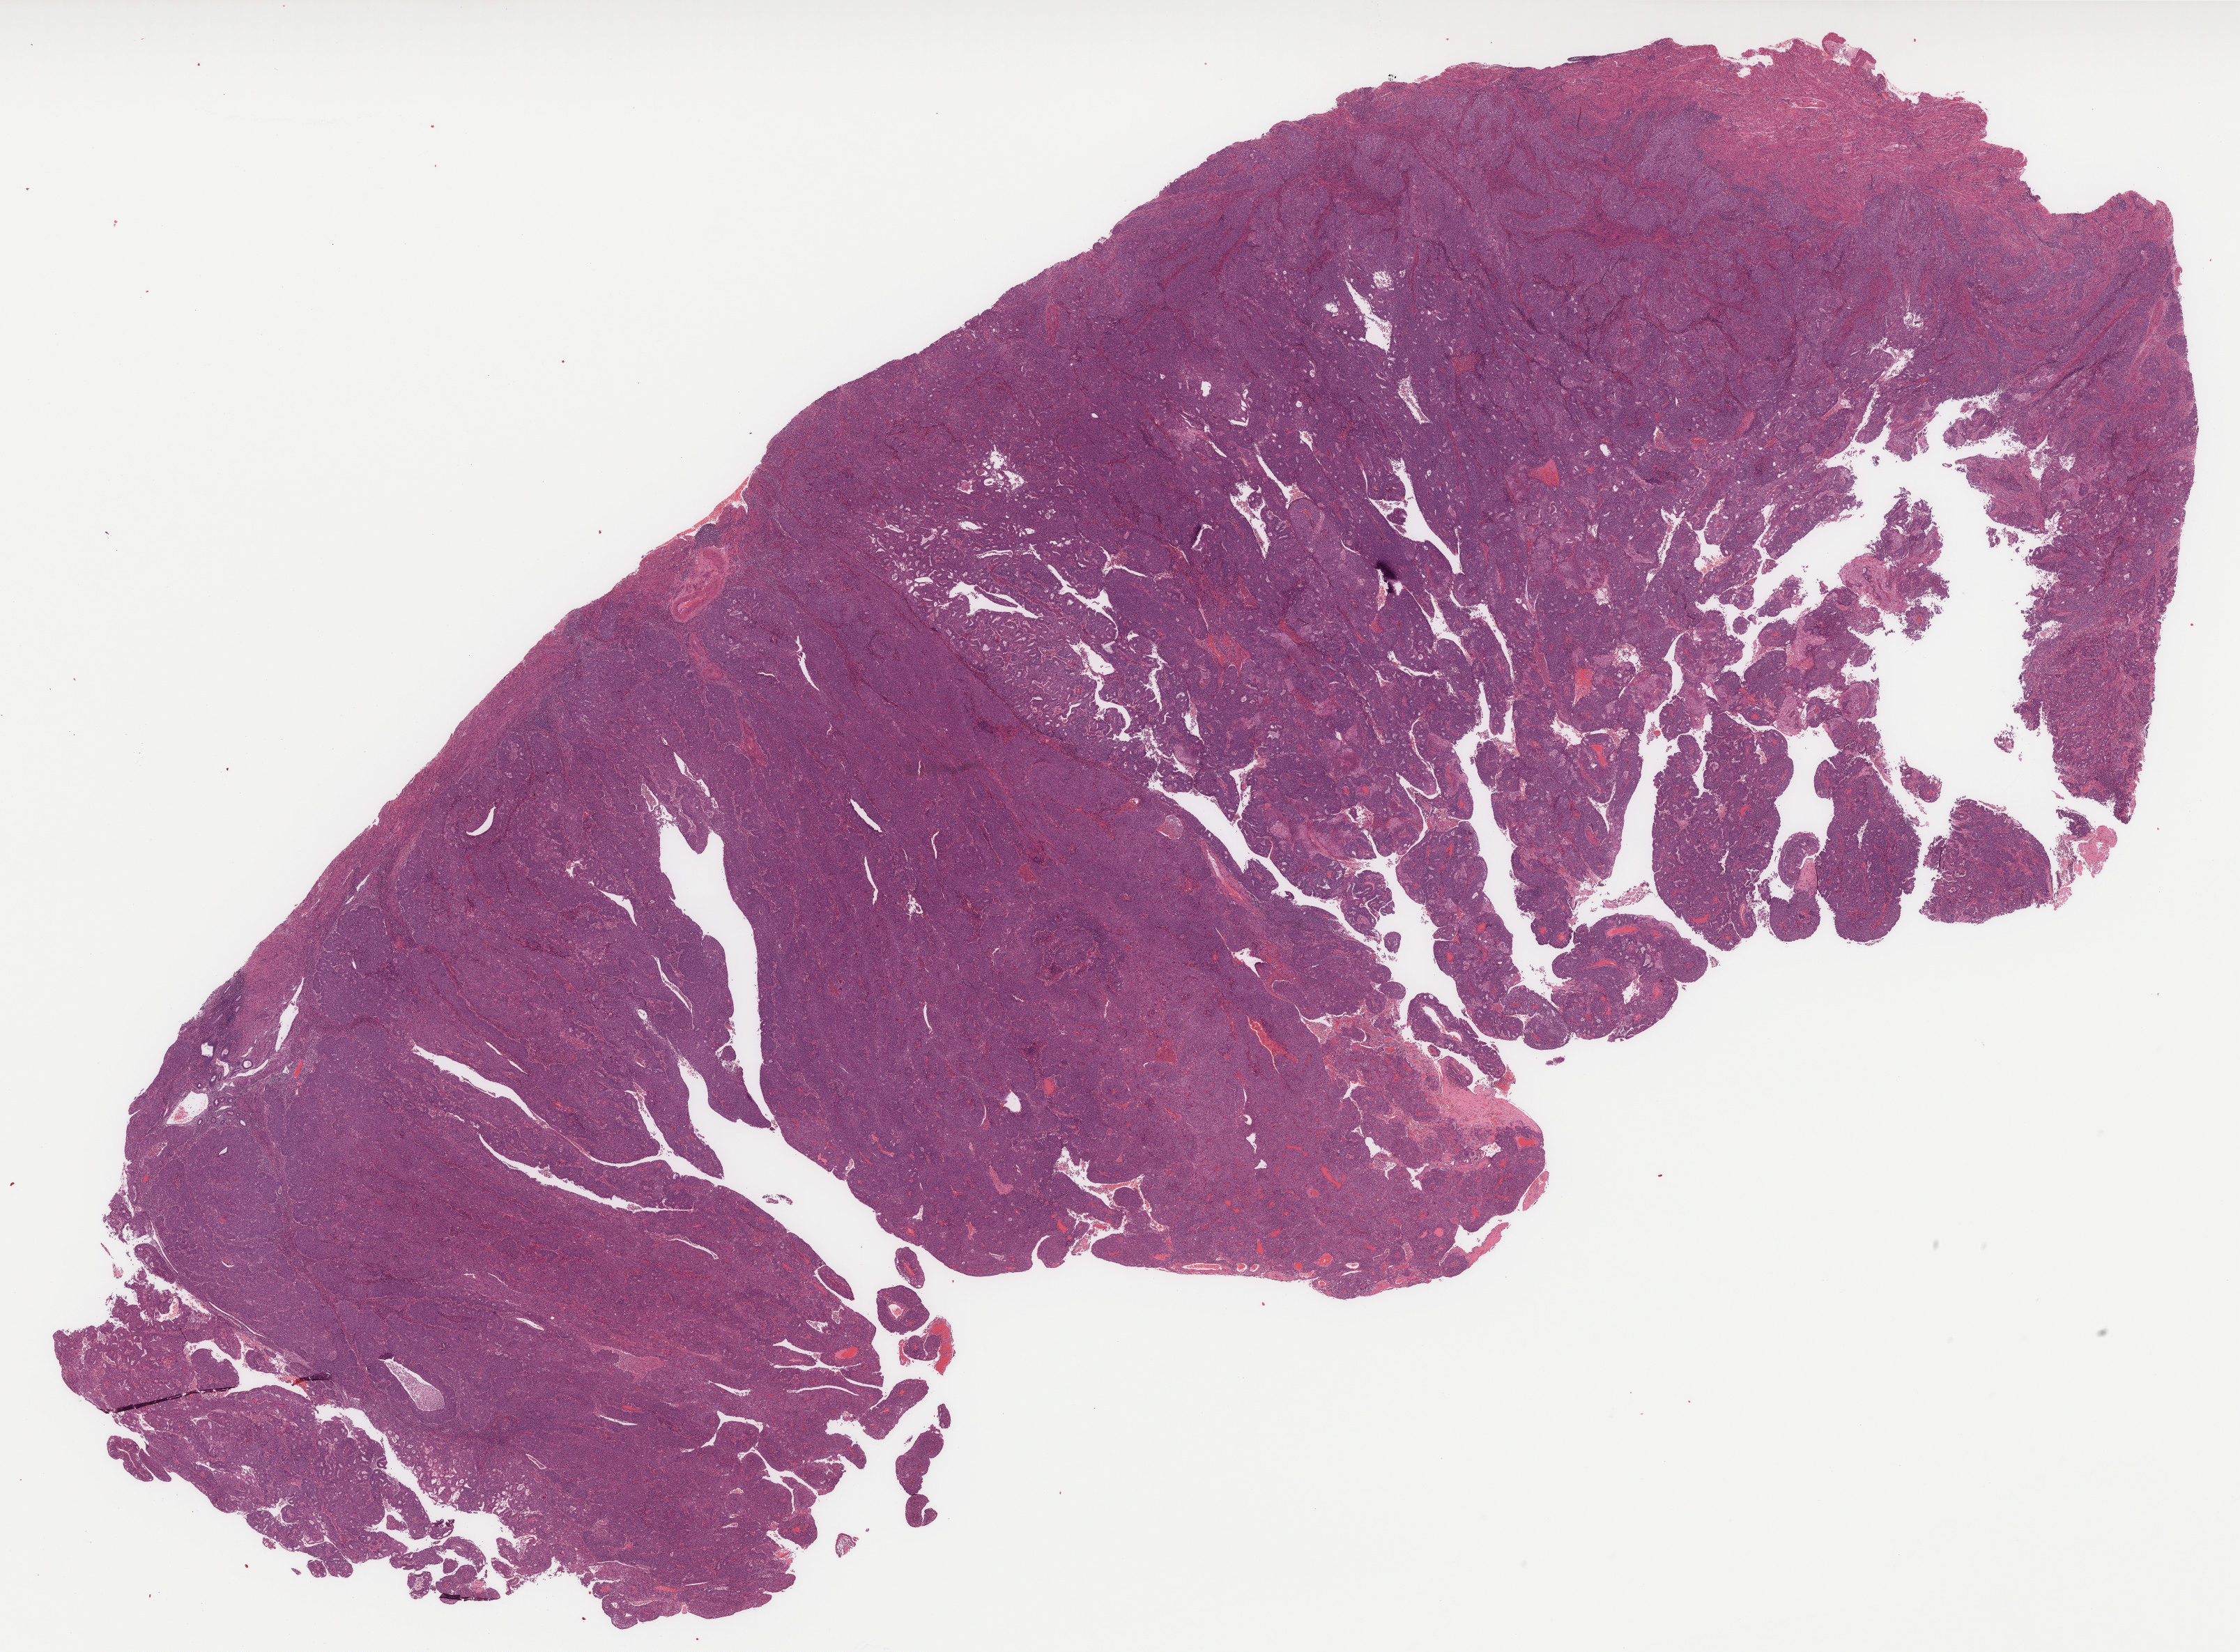
Digitized Hematoxylin and eosin (H&E) stained tissue section (whole slide), low-resolution overview of the scanned area, about 25.9 x 19.1 mm, FFPE section, sample: primary tumour, uterus. Female patient; age at initial diagnosis 58 years. Histologic grade: G3 (poorly differentiated).
• FIGO stage: IB
• pathologic diagnosis: Endometrioid adenocarcinoma, NOS (endometrium)